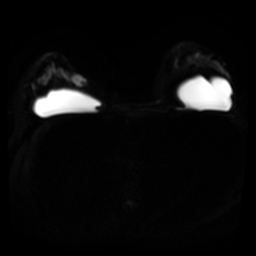
Breast MRI, one axial slice; position 28 of 45 along the scan axis; diffusion-weighted series; image 2 of 4 stored at this slice position (different b-values; order by instance number); 3 T; 256 × 256 image matrix, field of view 320 × 320 mm. Female patient.
Outlined on this slice (expert manual segmentation):
- tumour on diffusion-weighted imaging: box from (x=73, y=76) to (x=85, y=86) px